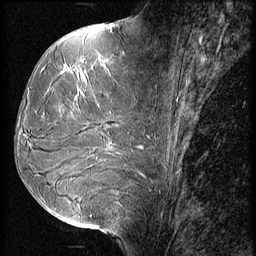
Breast MRI (dynamic contrast-enhanced), one sagittal slice. Slice 27 of 56 in the series (ordered by position). 3 images stored at this slice position (order not interpretable as contrast timing). 1.5 T. TE 4.2 ms, TR 9 ms. 2.5 mm slice thickness. 256 × 256 image matrix. Patient: female, 51 years. Case-level facts recorded for this patient, not image findings: setting: breast cancer imaged before/during neoadjuvant chemotherapy; receptor status: HR-positive, HER2-negative.
Outlined on this slice (semi-automatic segmentation, software-assisted and operator-edited):
- analysis volume of interest (the breast-tissue region the enhancement analysis was run in; not a lesion): box from (x=23, y=56) to (x=156, y=165) px
- tumour enhancement mask (voxels above the 140 % enhancement threshold inside the analysis volume of interest): (x=62, y=58)–(x=112, y=73)